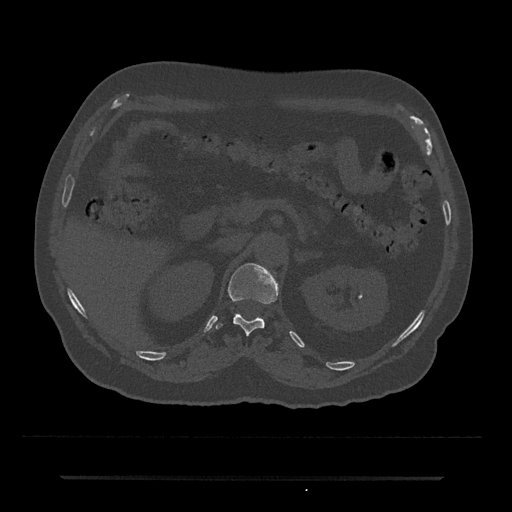
CT including the spine, one axial slice. Slice 122 of 797 in the series (ordered by position). 120 kVp. Bone window (W 1800 / L 400 HU). 0.5 mm slice thickness. 512 × 512 image matrix. Male patient, age 69 years. From the clinical record (not read from this slice): primary cancer: prostate.
Outlined on this slice (semi-automatically segmented with operator editing):
- T12 vertebra: box from (x=215, y=264) to (x=279, y=335) px